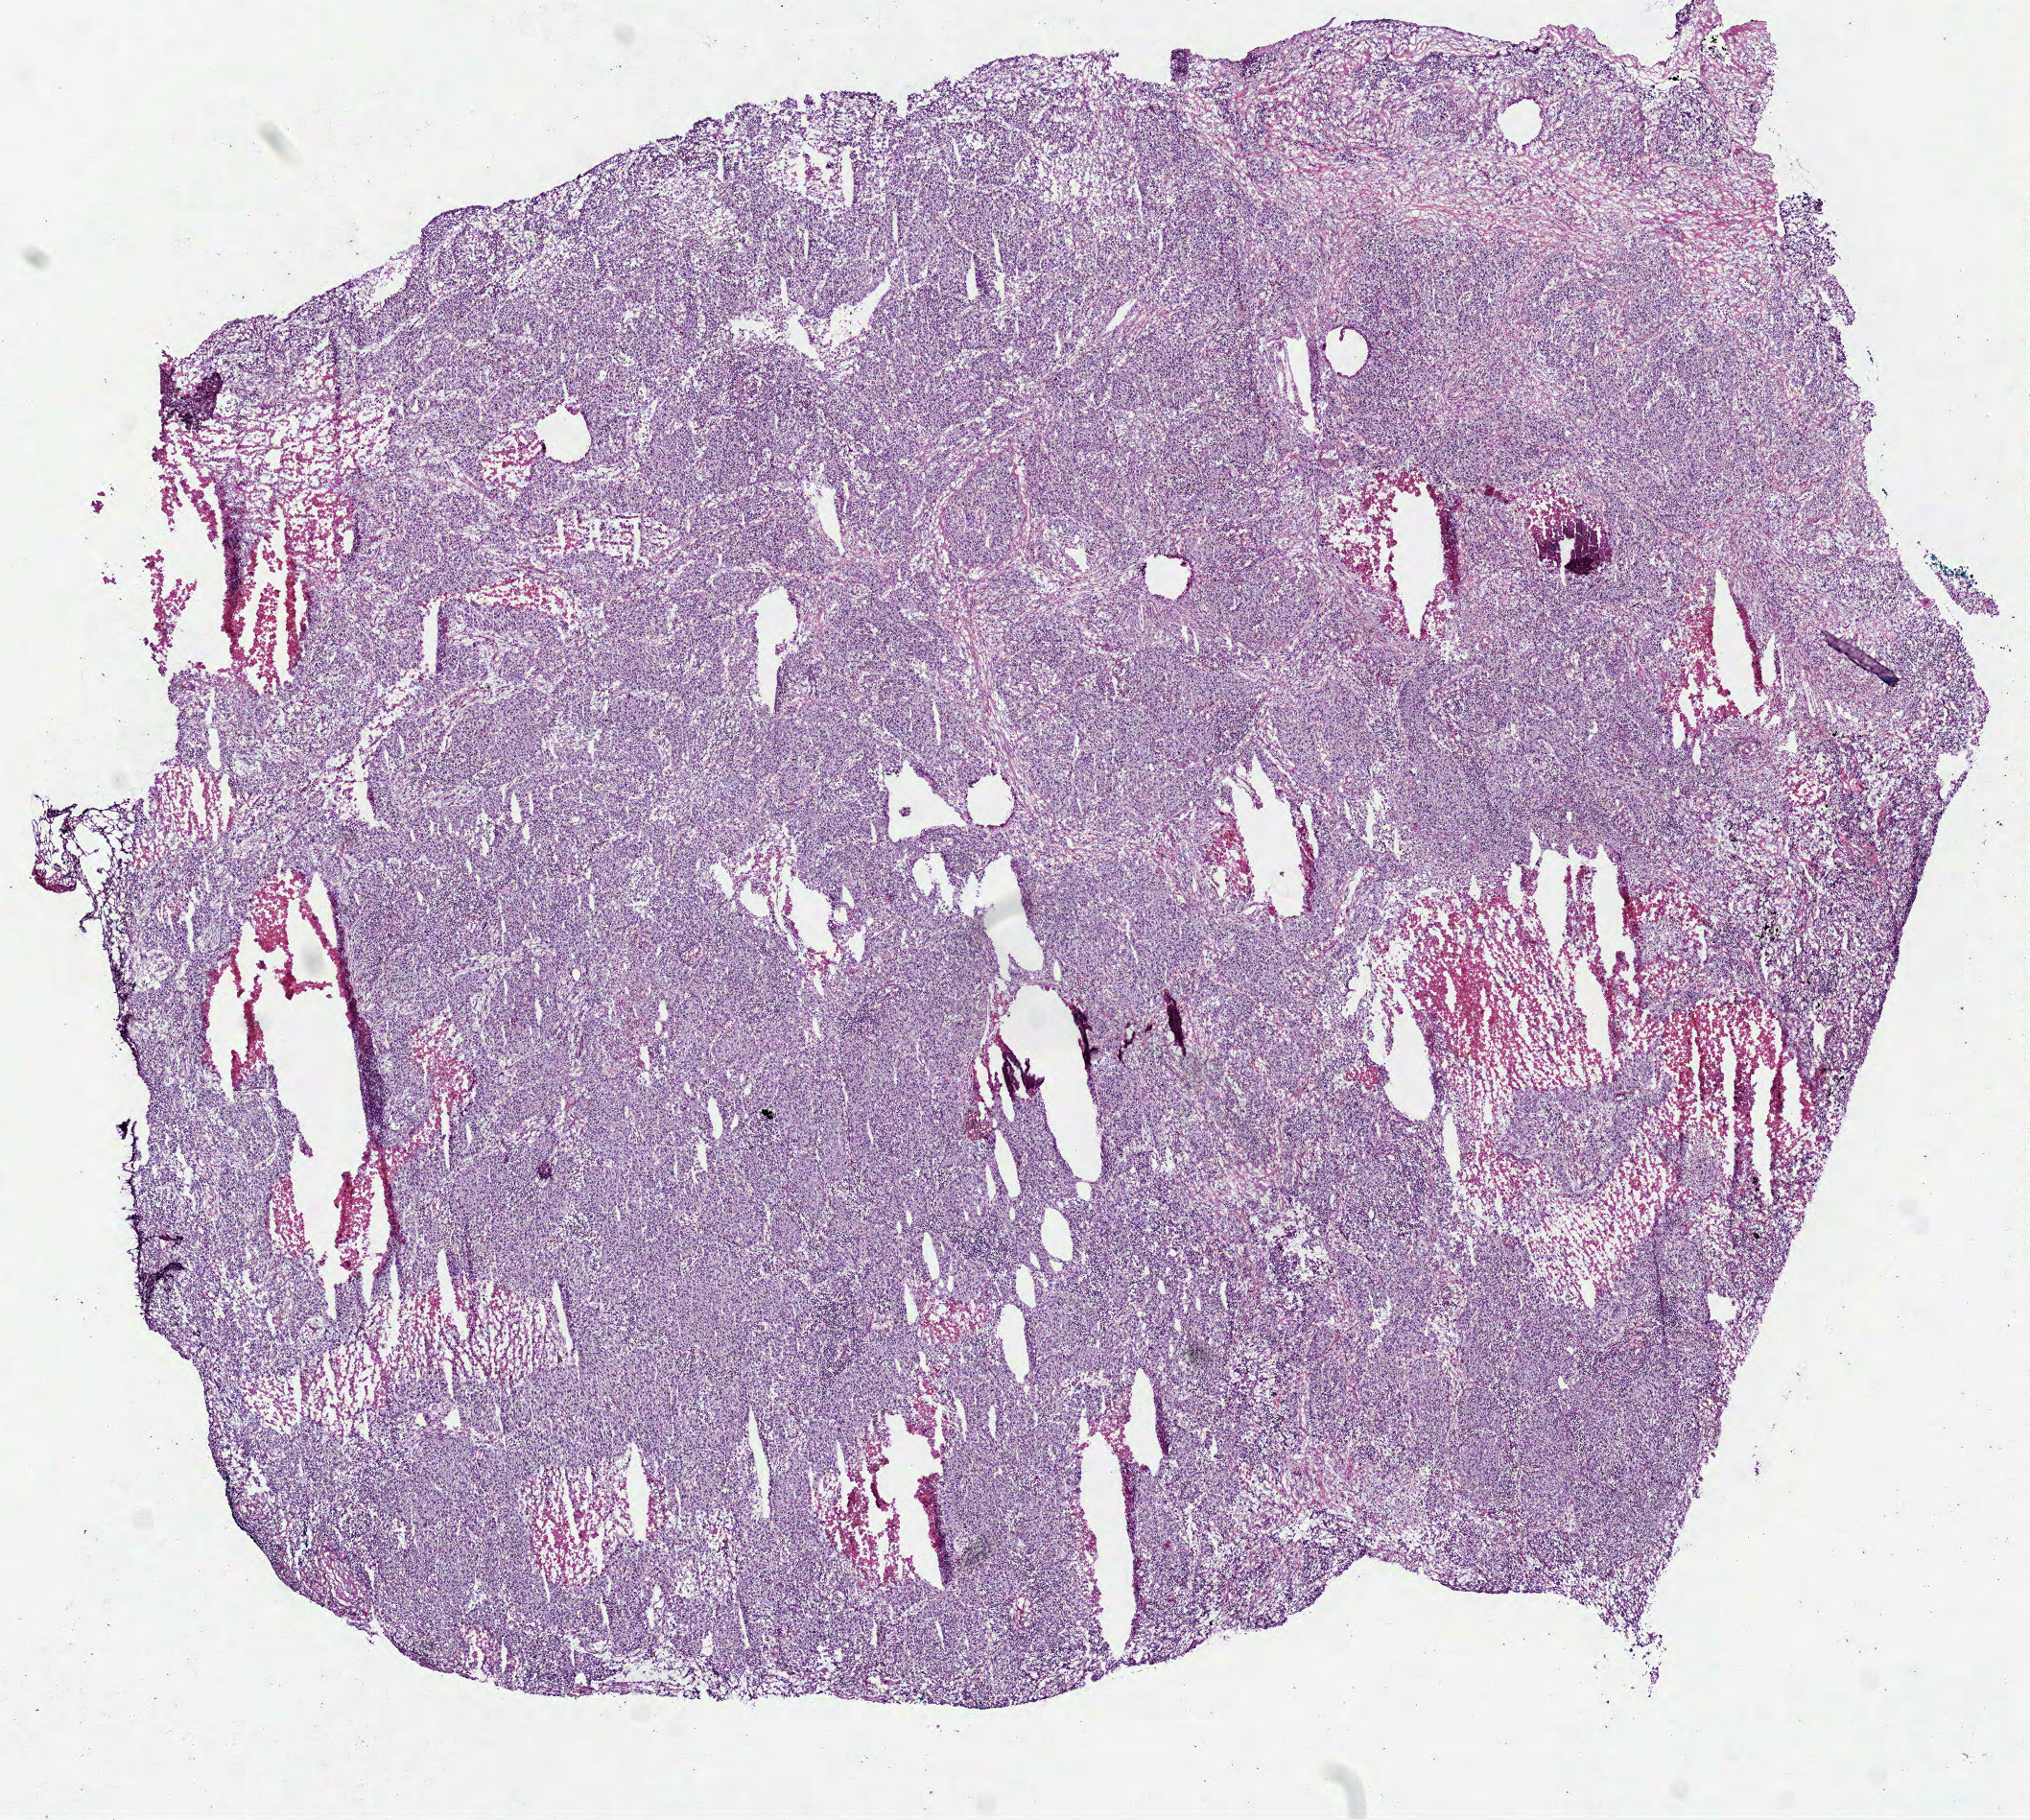
H&E whole-slide image, whole scanned area (about 8.5 x 7.7 mm, acquisition: 40x scan) shown as a low-resolution overview. Frozen section from the bottom of the tissue portion. Primary tumour sample from the lung. Female, age 73 years at initial diagnosis.
Histologic diagnosis: Adenocarcinoma, NOS (upper lobe, lung).